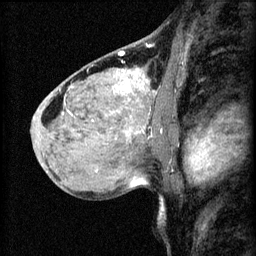
Breast MRI (dynamic contrast-enhanced), one sagittal slice. Slice 41 of 60 in the series (ordered by position). 3 images stored at this slice position (order not interpretable as contrast timing). 1.5 T. TE 4.2 ms, TR 8.2 ms. 2.2 mm slice thickness. 256 × 256 image matrix. Patient: female, 40 years.
Outlined on this slice (semi-automatically segmented with operator editing):
- analysis volume of interest (the breast-tissue region the enhancement analysis was run in; not a lesion): bounding box [x1, y1, x2, y2] px = [108, 82, 175, 139]
- tumour enhancement mask (voxels above the 70 % enhancement threshold inside the analysis volume of interest): [112, 82, 163, 137]